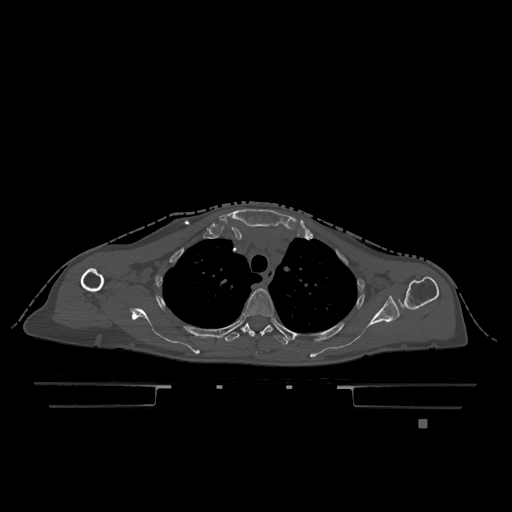
CT including the spine, one axial slice. Slice 905 of 1317 in the series (ordered by position). Bone window (W 1800 / L 400 HU). 0.5 mm slice thickness. 512 × 512 image matrix, field of view 500 × 500 mm. Female patient, age 74 years. From the clinical record (not read from this slice): primary cancer: lung; vertebrae with lytic lesions (as recorded): T1, T4, T5, T6, L4, L5.
Structures marked on this image (semi-automatic segmentation, software-assisted and operator-edited):
- T3 vertebra: bounding box <245,288,274,353> (left, top, right, bottom; pixels)
- T4 vertebra: <225,323,296,345>